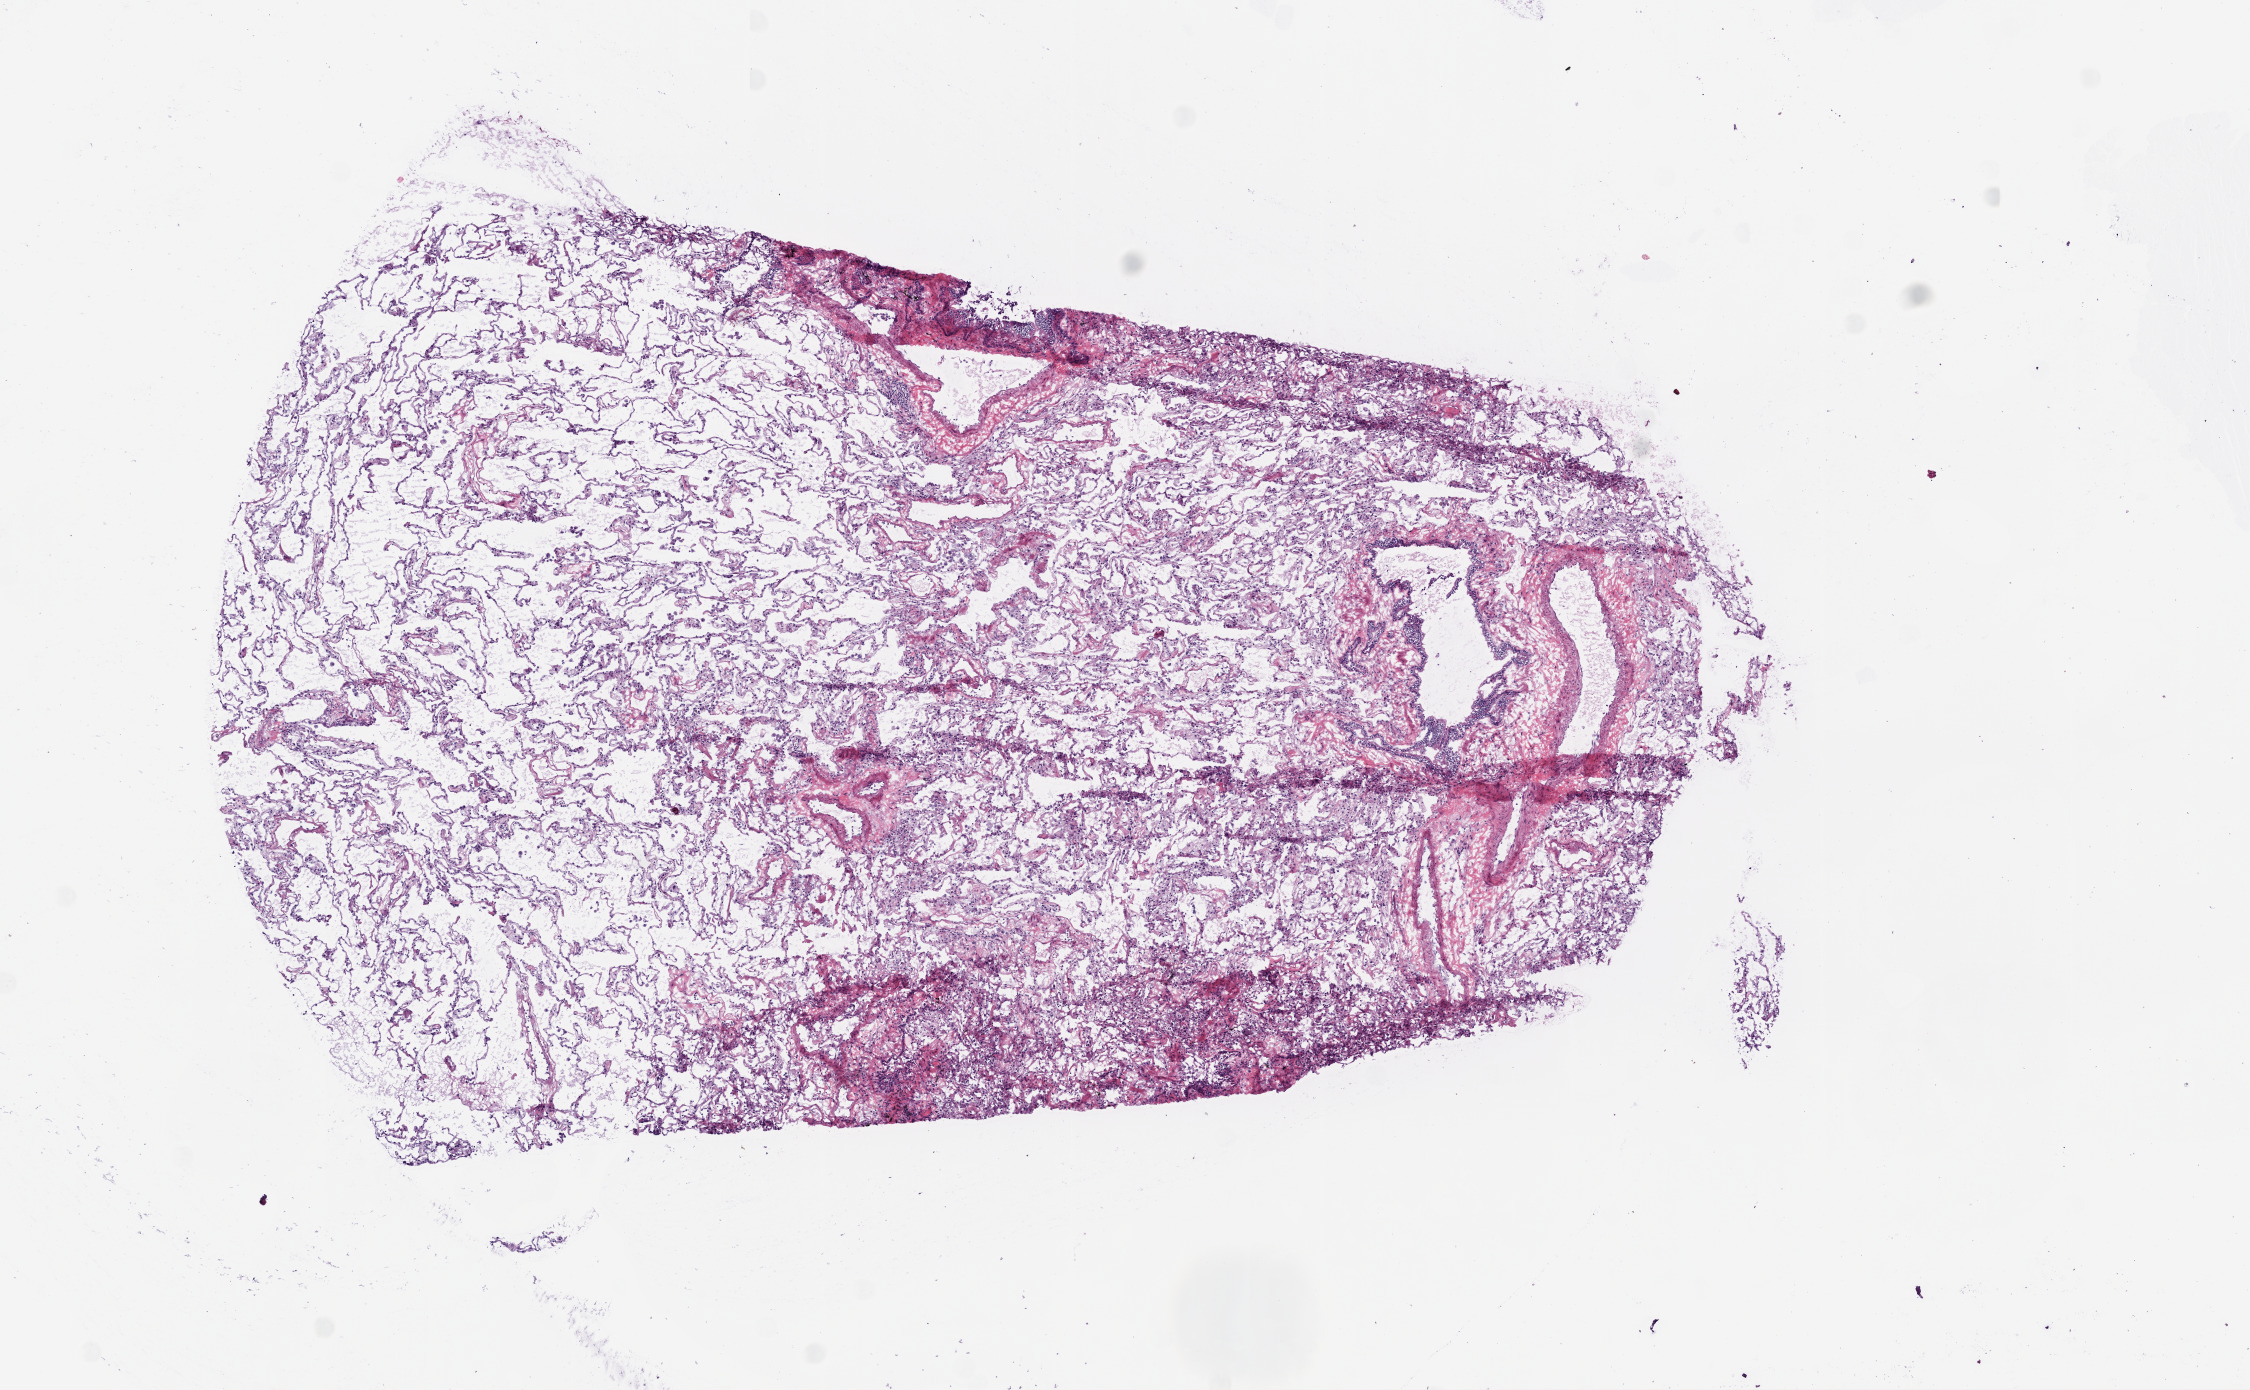
Whole-slide histology image, H&E — whole scanned area (about 9.0 x 5.6 mm) shown as a low-resolution overview, frozen section from the bottom of the tissue portion, sample: solid tissue normal (non-tumour tissue), lung. Male patient; age at initial diagnosis 77 years.
* this section: solid tissue normal sample (biorepository sample class)
* patient diagnosis: Squamous cell carcinoma, NOS (upper lobe, lung)